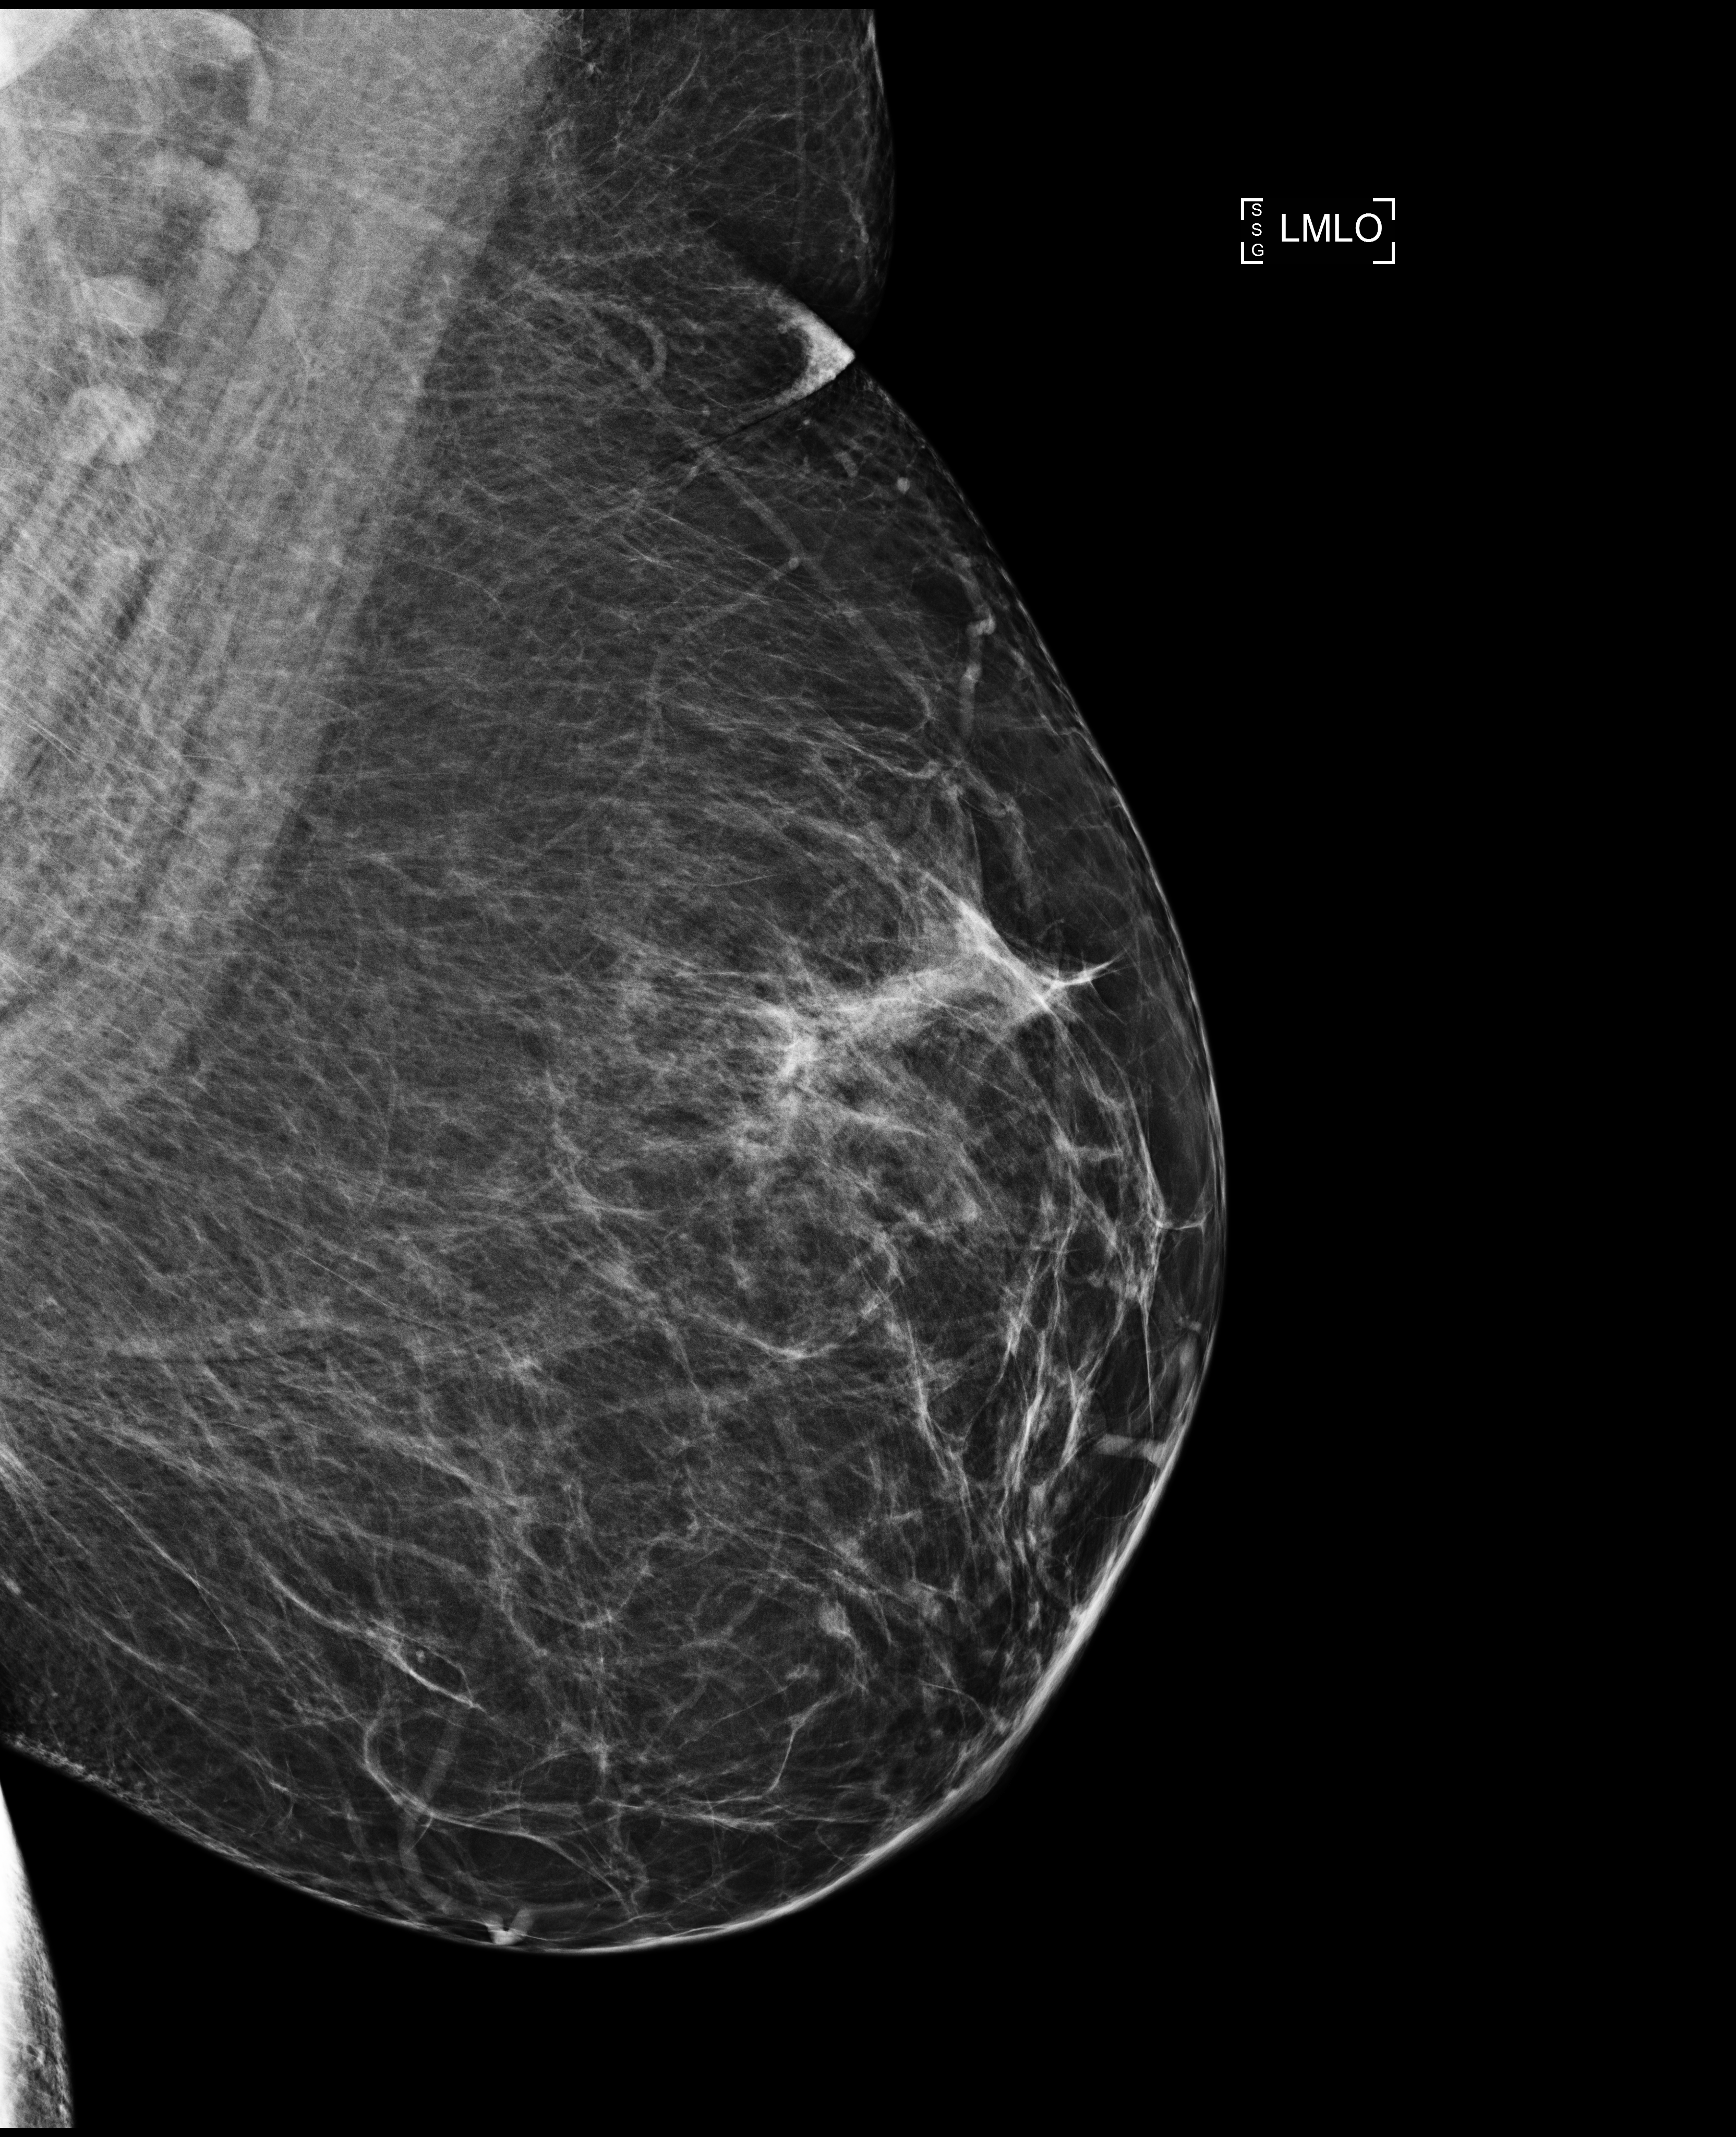
Full-field digital mammogram (FFDM), left breast, medio-lateral oblique projection, annual screening mammography examination. Female patient, age 51 years.
- breast density at the screening exam (both breasts): scattered fibroglandular densities (BI-RADS density category b)
- final BI-RADS assessment for this screening round (tomosynthesis exam, both breasts): category 2
- recall: no recall after this screen